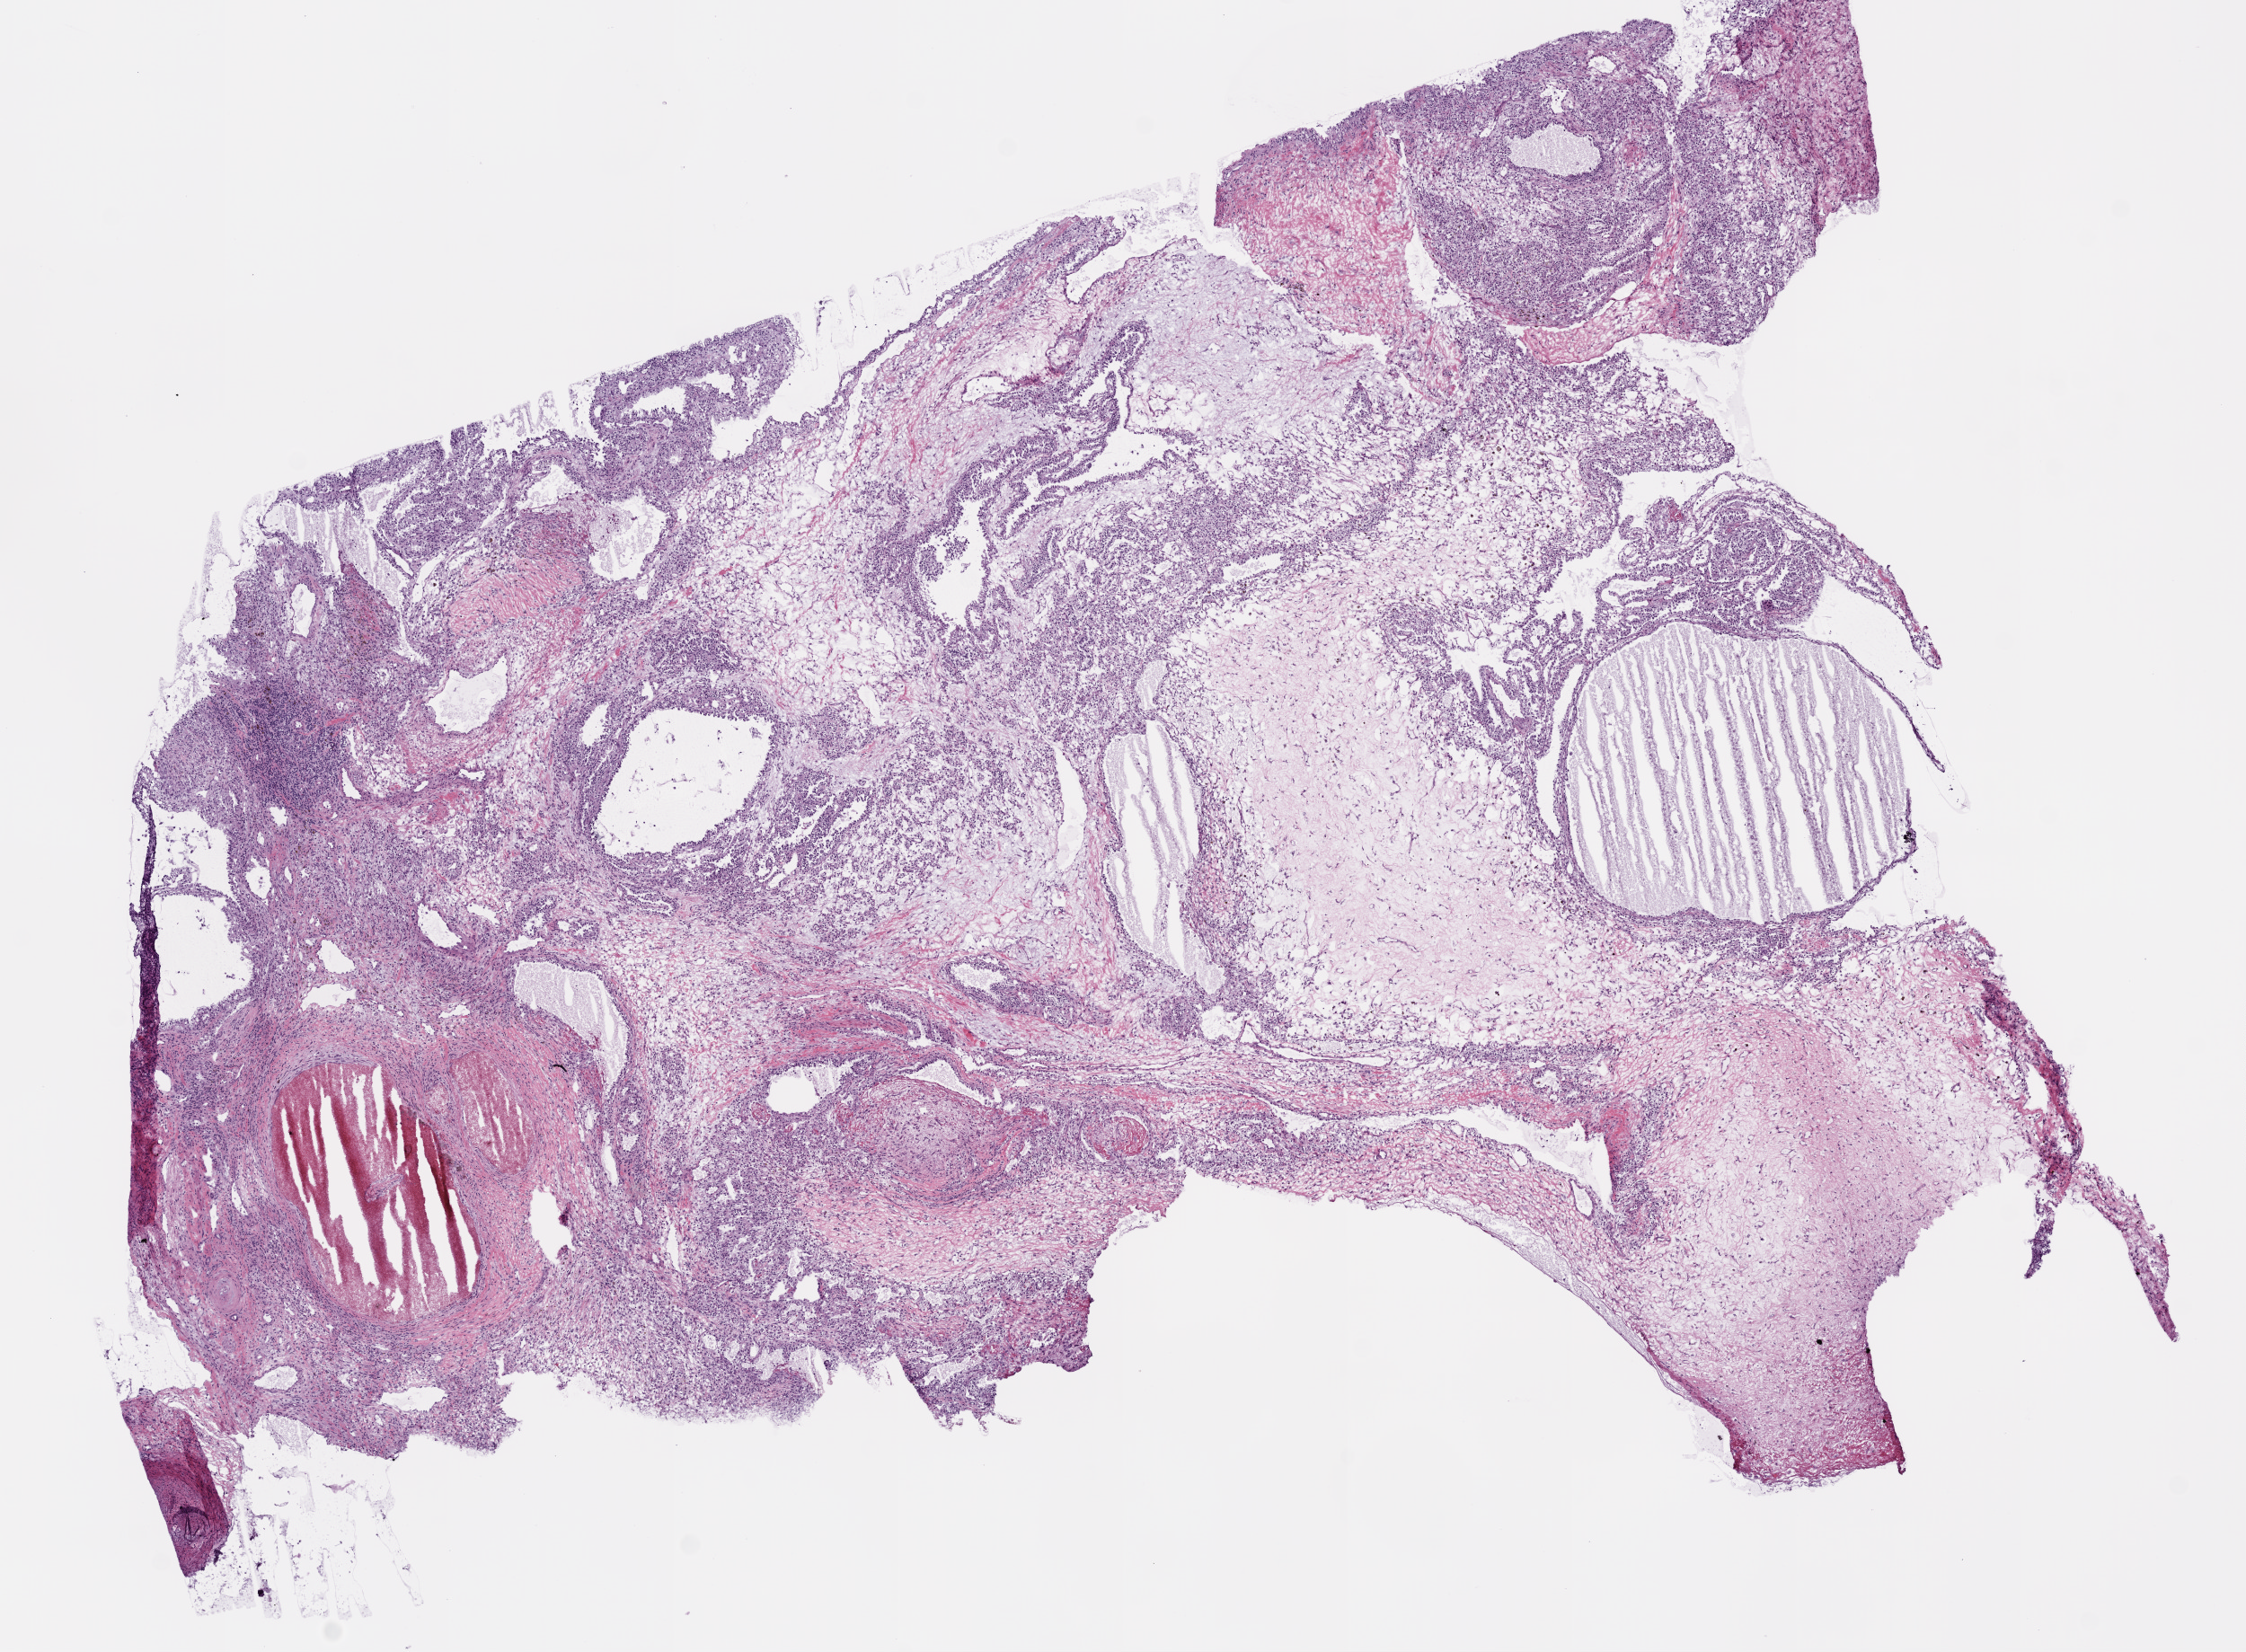
H&E whole-slide image, low-resolution overview of the scanned area, about 10.0 x 7.4 mm. Frozen section. Primary tumour sample from the kidney. Patient: male, age at initial diagnosis 42 years. Histologic grade: G2 (moderately differentiated). Slide review estimates, as recorded: tumour nuclei 75%, normal cells 0%, stromal cells 60%, necrosis 0%.
- laterality: left
- diagnosis: Clear cell adenocarcinoma, NOS
- AJCC pathologic stage: I (7th edition)